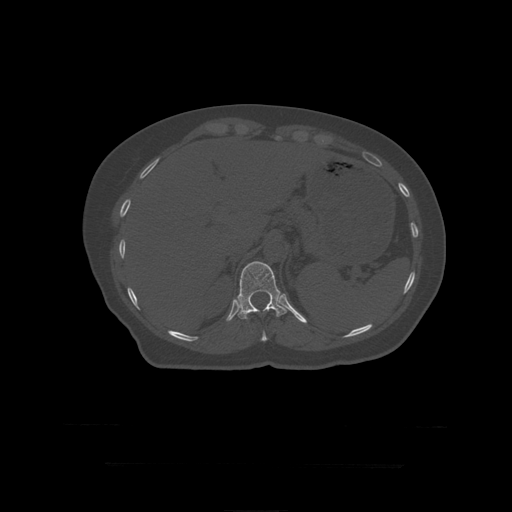
CT including the spine, one axial slice. Reconstruction kernel STANDARD. 120 kVp. Bone window (W 1800 / L 400 HU). 512 × 512 image matrix, field of view 450 × 450 mm. Patient age 41 years. From the clinical record (not read from this slice): primary cancer: breast.
Structures marked on this image (semi-automatically segmented with operator editing):
- T11 vertebra: bounding box <261,331,268,342> (left, top, right, bottom; pixels)
- T12 vertebra: <238,261,288,320>